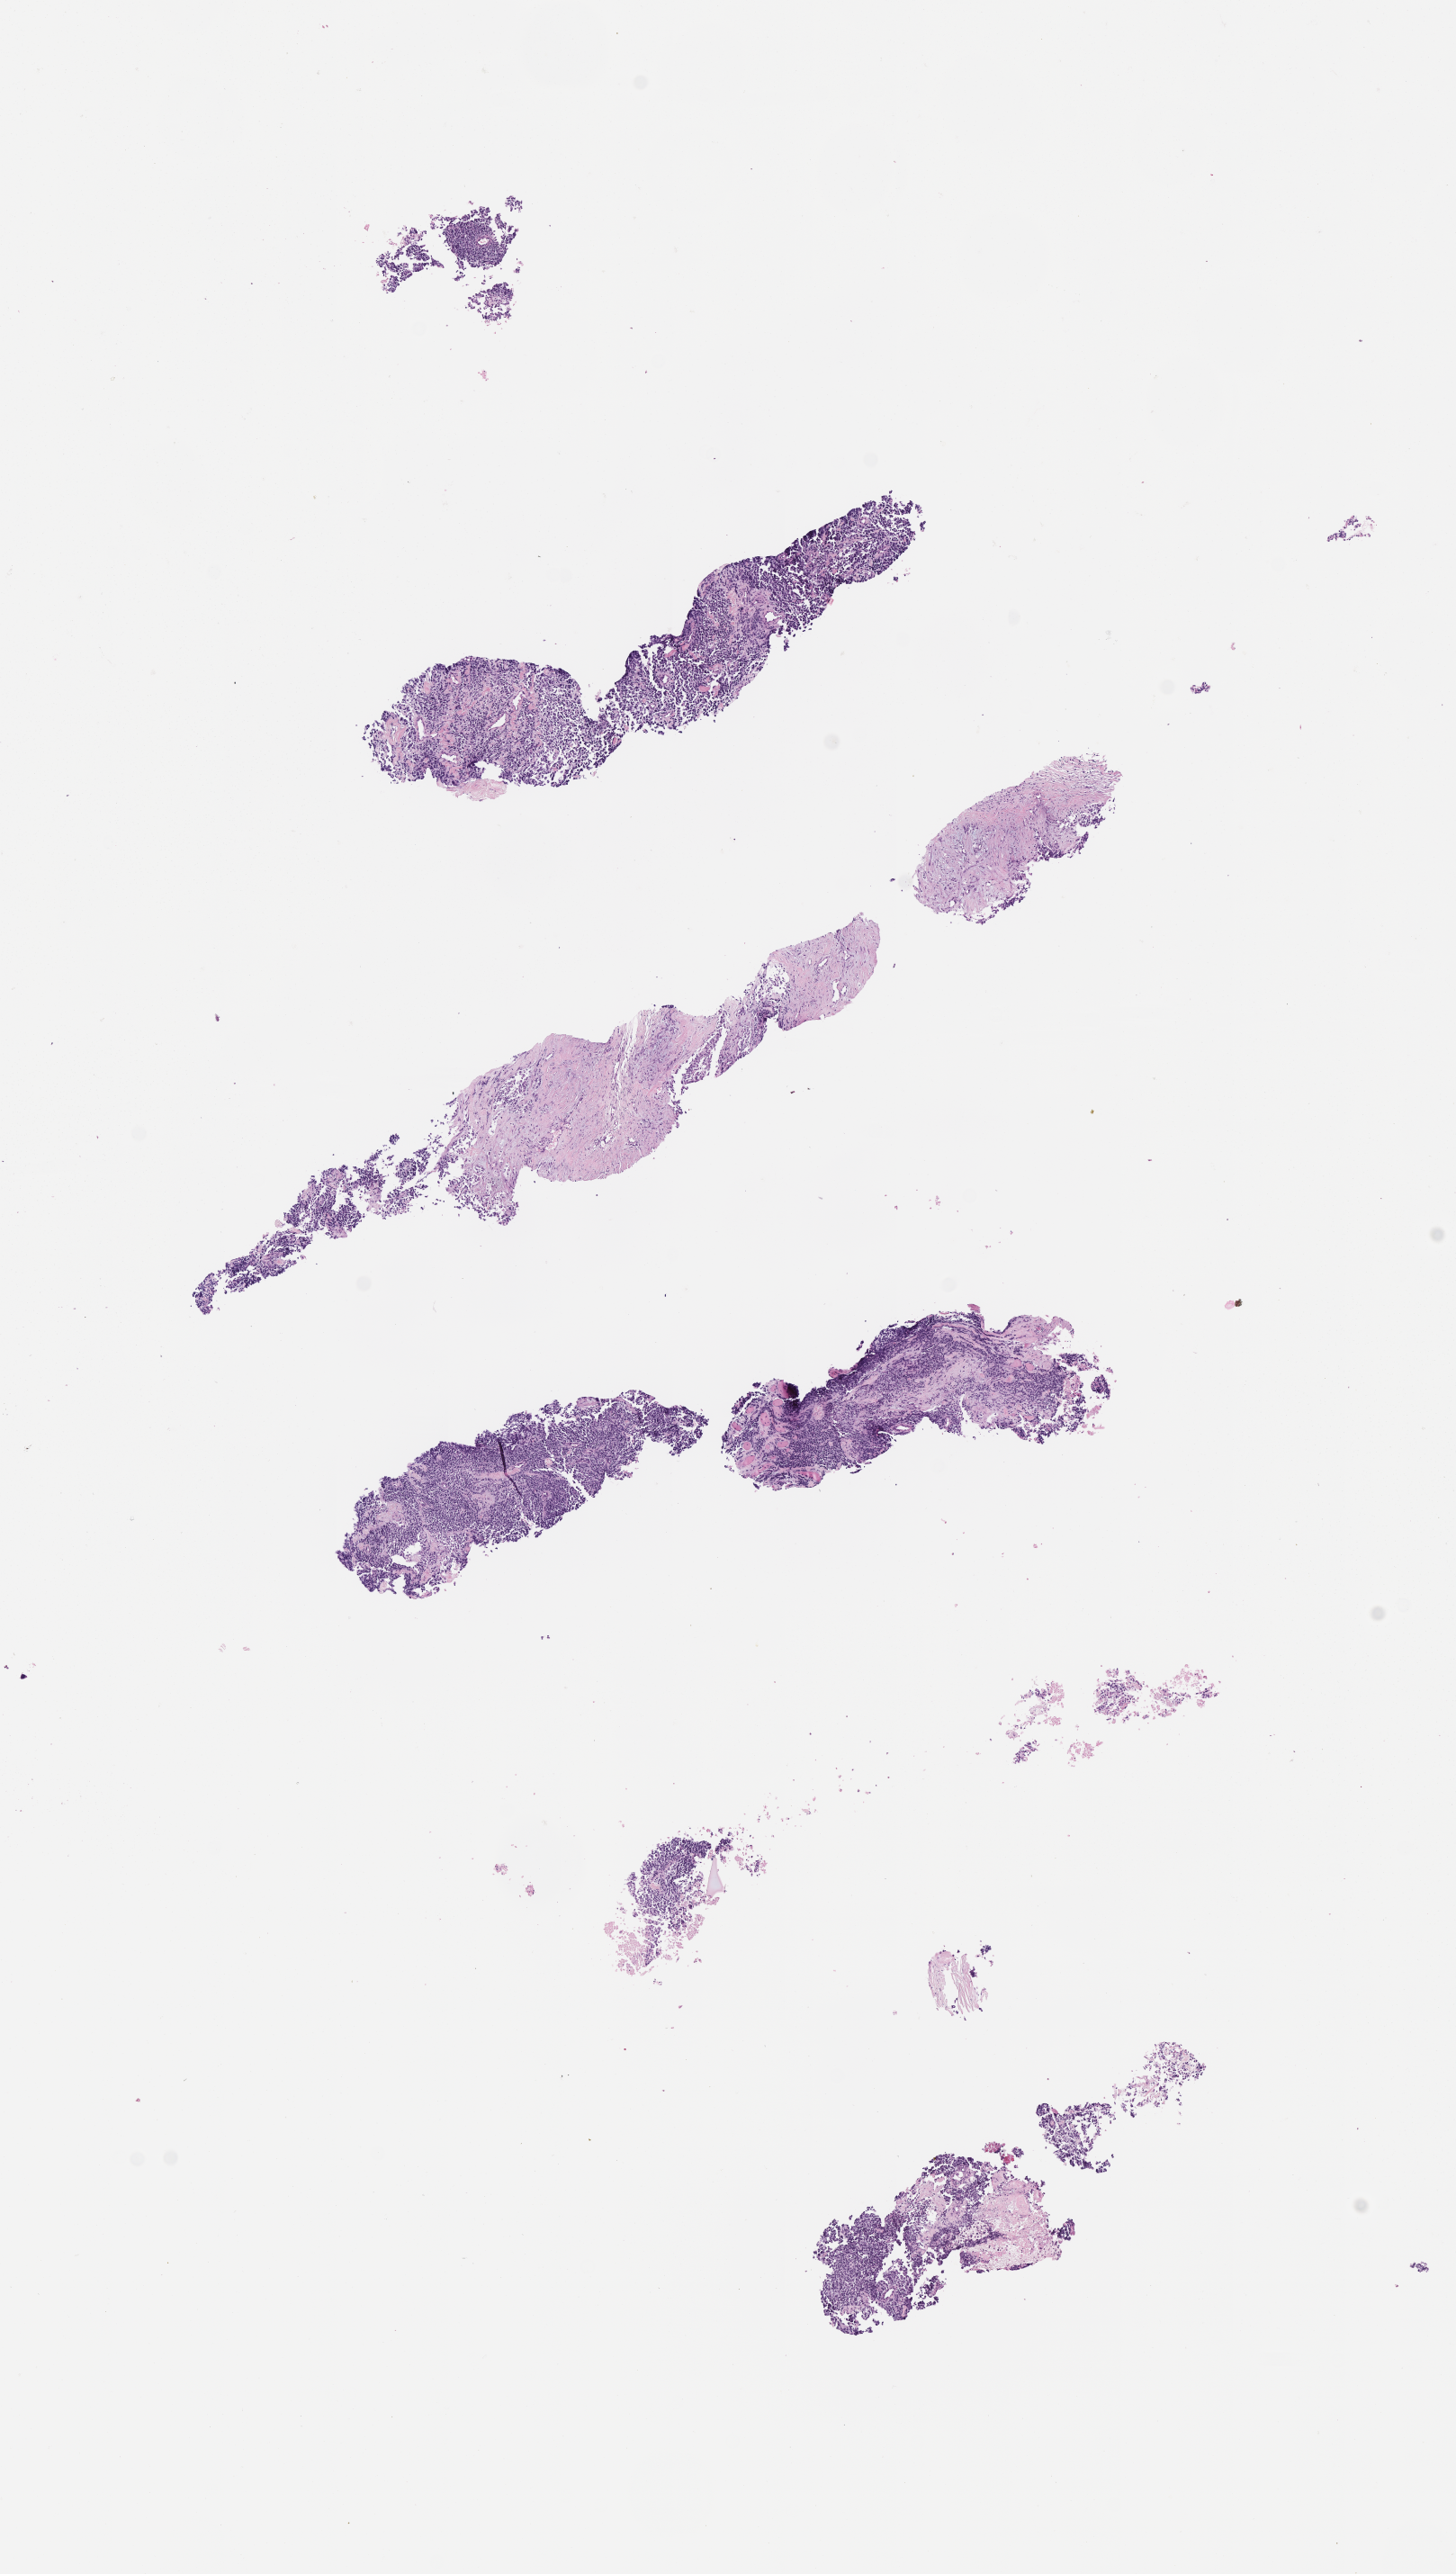
H&E whole-slide image of tumor tissue, low-resolution overview of the scanned area, about 6.5 x 11.6 mm, FFPE section, site: peritoneum. Patient: female, age 16.6 years at diagnosis.
Diagnosis: rhabdomyosarcoma; histological classification: alveolar rhabdomyosarcoma.